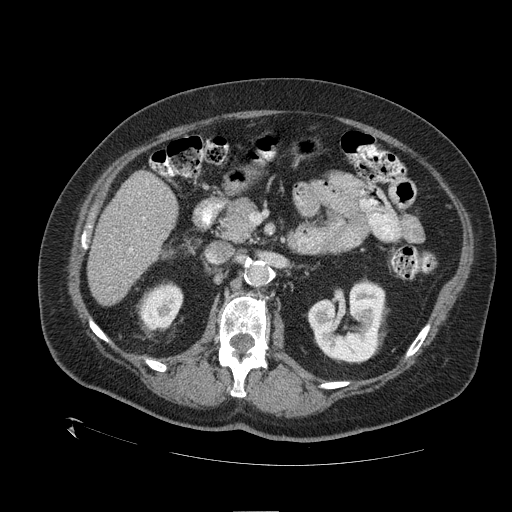
Contrast-enhanced abdominal CT (liver protocol), one axial slice. Reconstruction kernel STANDARD. 120 kVp. One of 2 acquisitions stored at this slice position. Soft-tissue window (W 400 / L 40 HU). 2.5 mm slice thickness. 512 × 512 image matrix, field of view 460 × 460 mm. From the clinical record (not read from this slice): diagnosis: hepatocellular carcinoma (patient treated with transarterial chemoembolisation; whether this scan precedes or follows treatment is not stated here); TNM stage (as recorded): Stage-I; Child-Pugh class: A; tumour nodularity: uninodular.
Annotated regions visible in this slice (semi-automatic segmentation, software-assisted and operator-edited):
- liver parenchyma outside the tumour (the mass and vessels are separate outlines, so this box may not span the whole liver): bounding box [x1, y1, x2, y2] px = [88, 170, 178, 306]
- liver vessels: [129, 218, 144, 252]